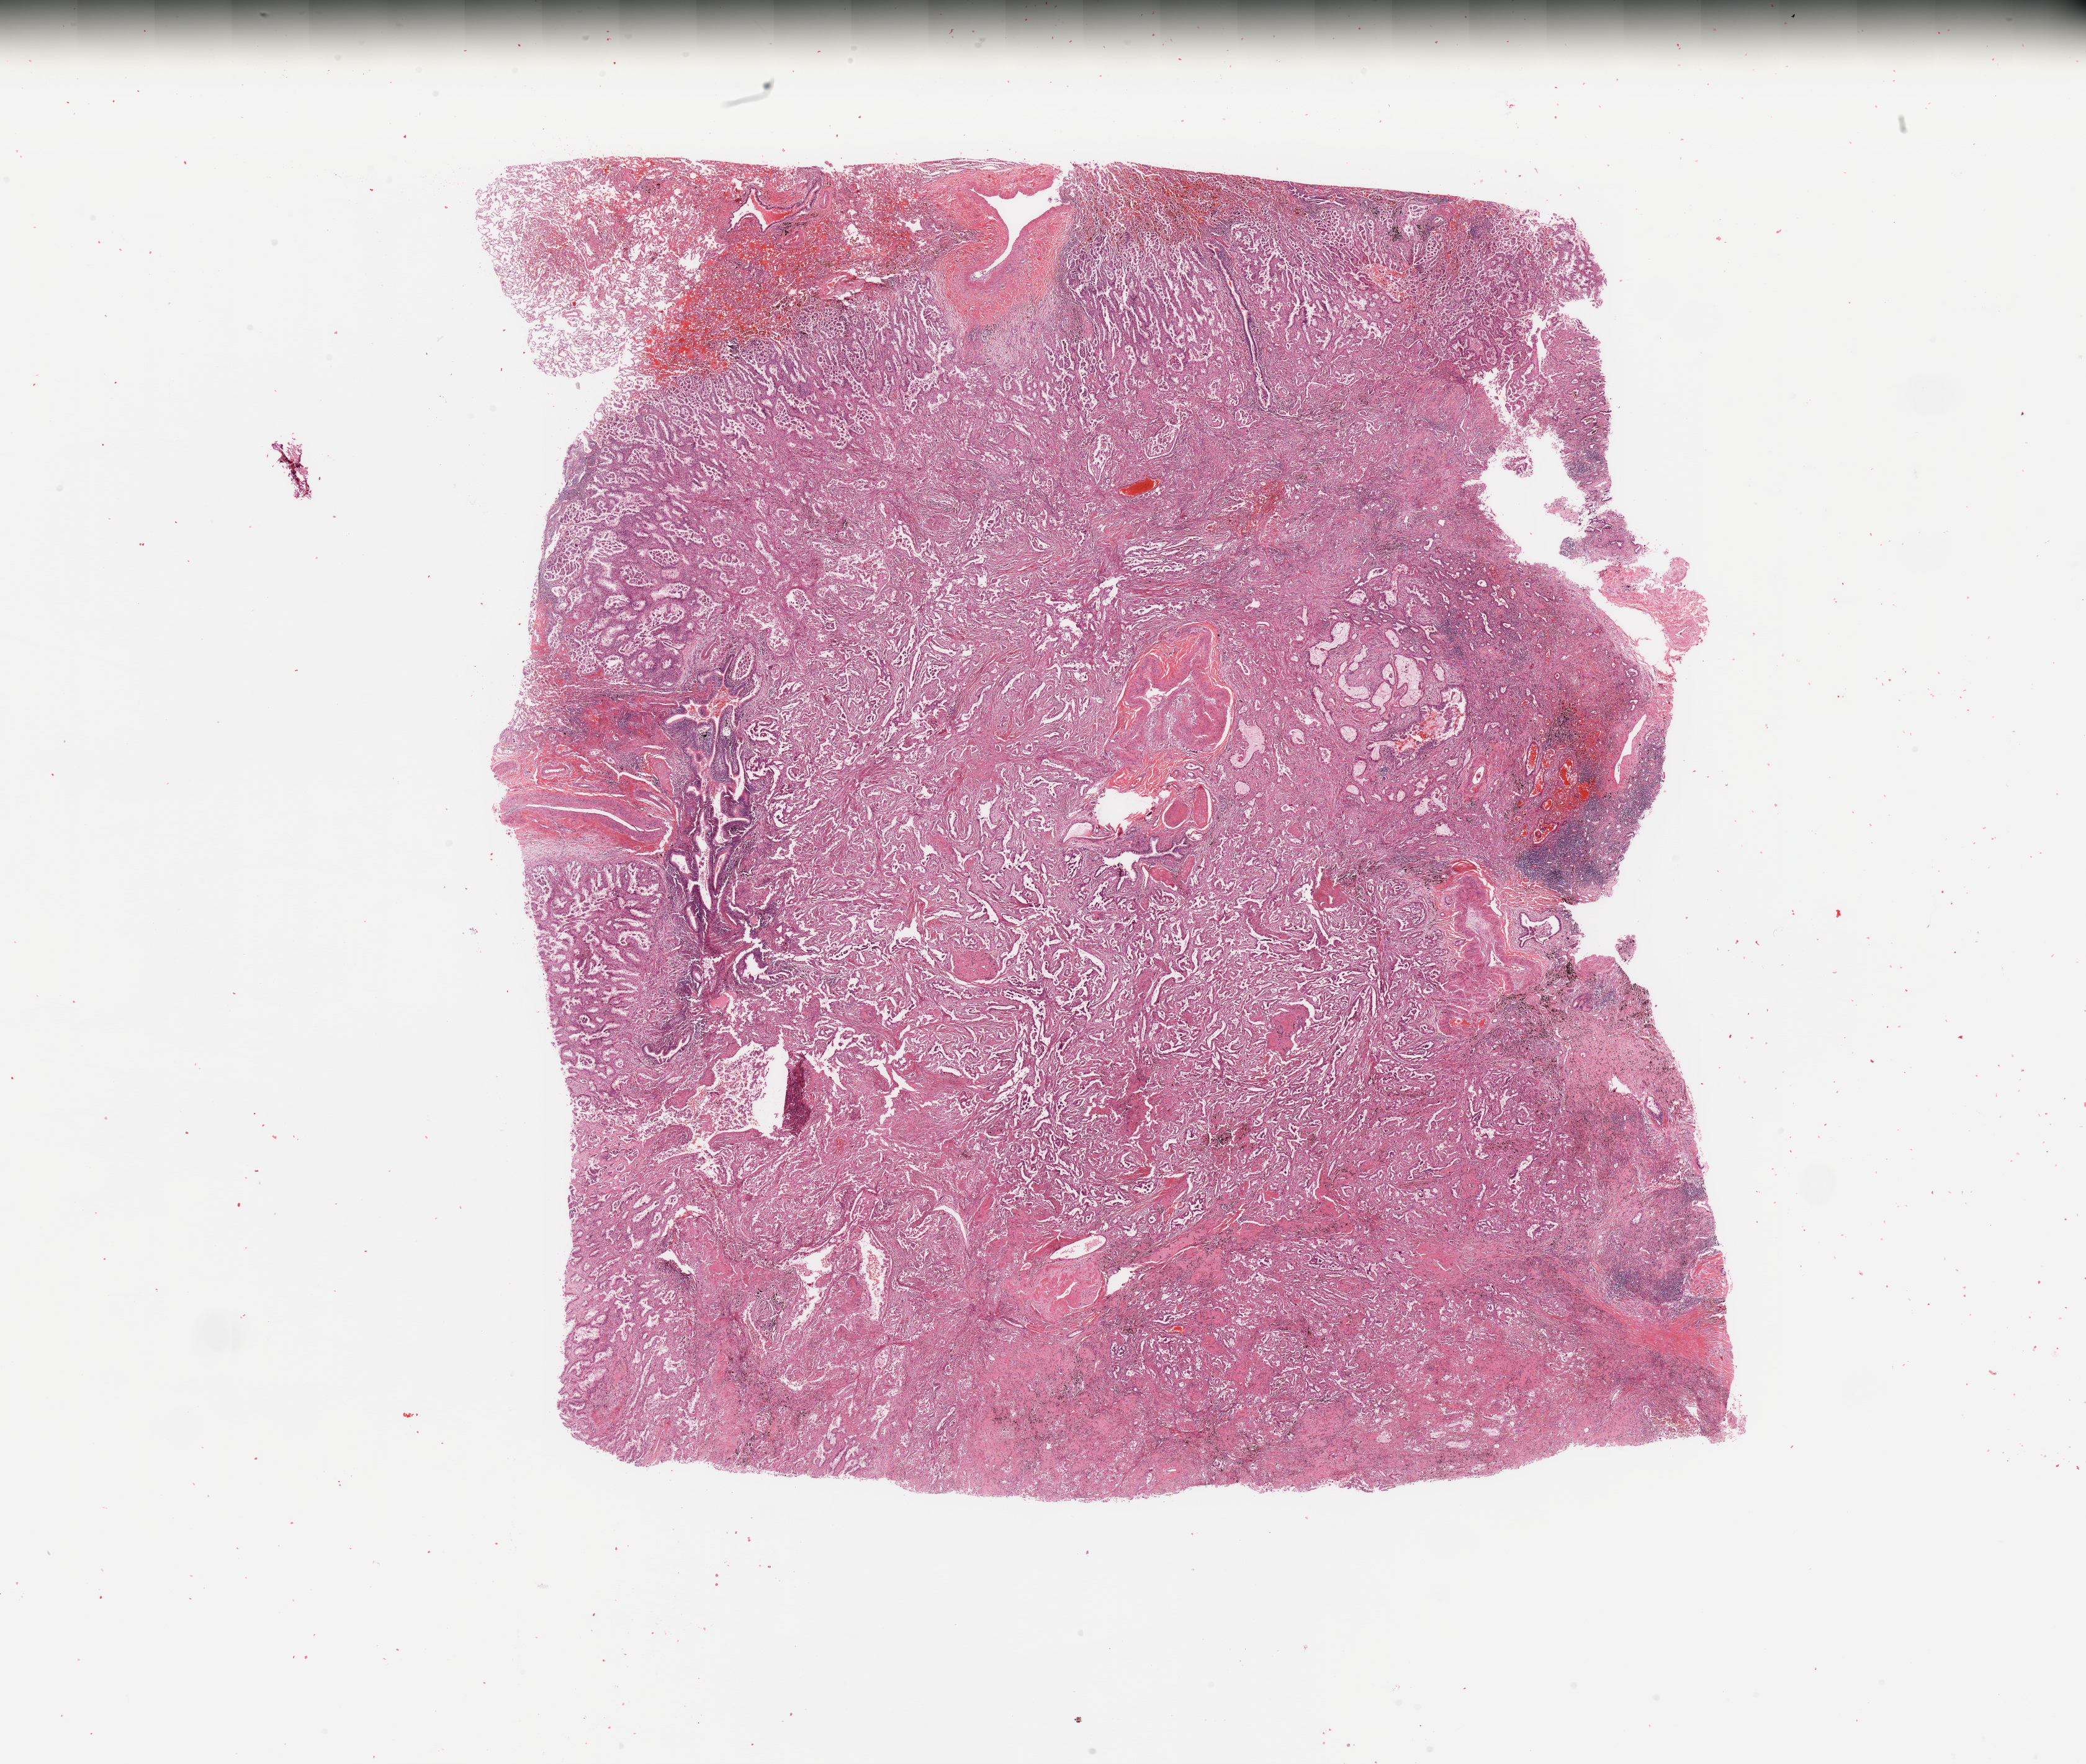
Digitized H&E tissue section (whole slide), a low-resolution overview of the entire scanned area, about 26.6 x 22.5 mm (slide scanned at 20x), tumour tissue sample, sampled site: lung. Patient: male, age 60 years. Histologic grade: G2 (moderately differentiated). Composition of this section per pathologist review: tumour nuclei 70%, necrosis 2%.
- histologic diagnosis: Adenocarcinoma, NOS
- AJCC pathologic stage: IIB